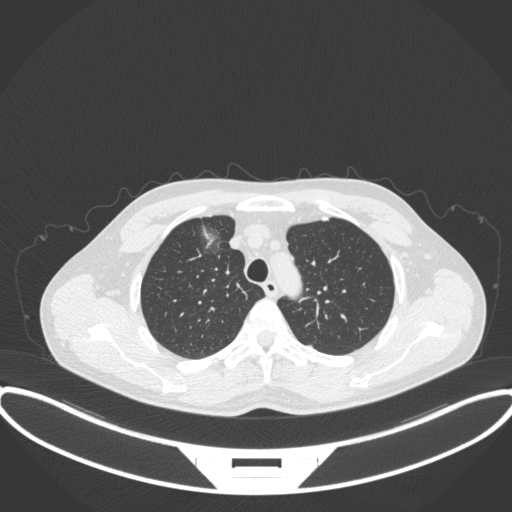
Chest CT, one axial slice. Position 288 of 395 along the scan axis. 120 kVp. Lung window (W 1500 / L -600 HU). 1 mm slice thickness. 512 × 512 image matrix, field of view 424 × 424 mm. Patient: male, 60 years. From the clinical record (not read from this slice): clinical TNM (as recorded): T1c N0 M0.
Structures marked on this image (bounding box drawn by a radiologist):
- lung tumour (recorded histology: adenocarcinoma): bounding box [x1, y1, x2, y2] px = [195, 219, 229, 264]